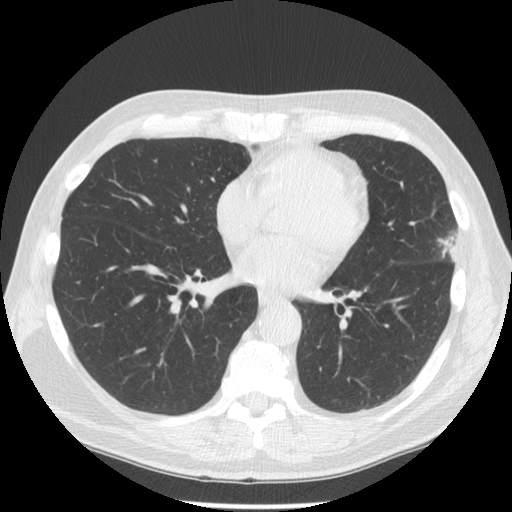
Low-dose screening chest CT, one axial slice. Position 63 of 134 along the scan axis. Reconstruction kernel STANDARD. Lung window (W 1500 / L -600 HU). 2.5 mm slice thickness. 512 × 512 image matrix, field of view 350 × 350 mm.
Structures marked on this image (expert manual segmentation):
- lesion 1 (tumor, upper lobe of left lung): bounding box <438,233,457,260> (left, top, right, bottom; pixels)